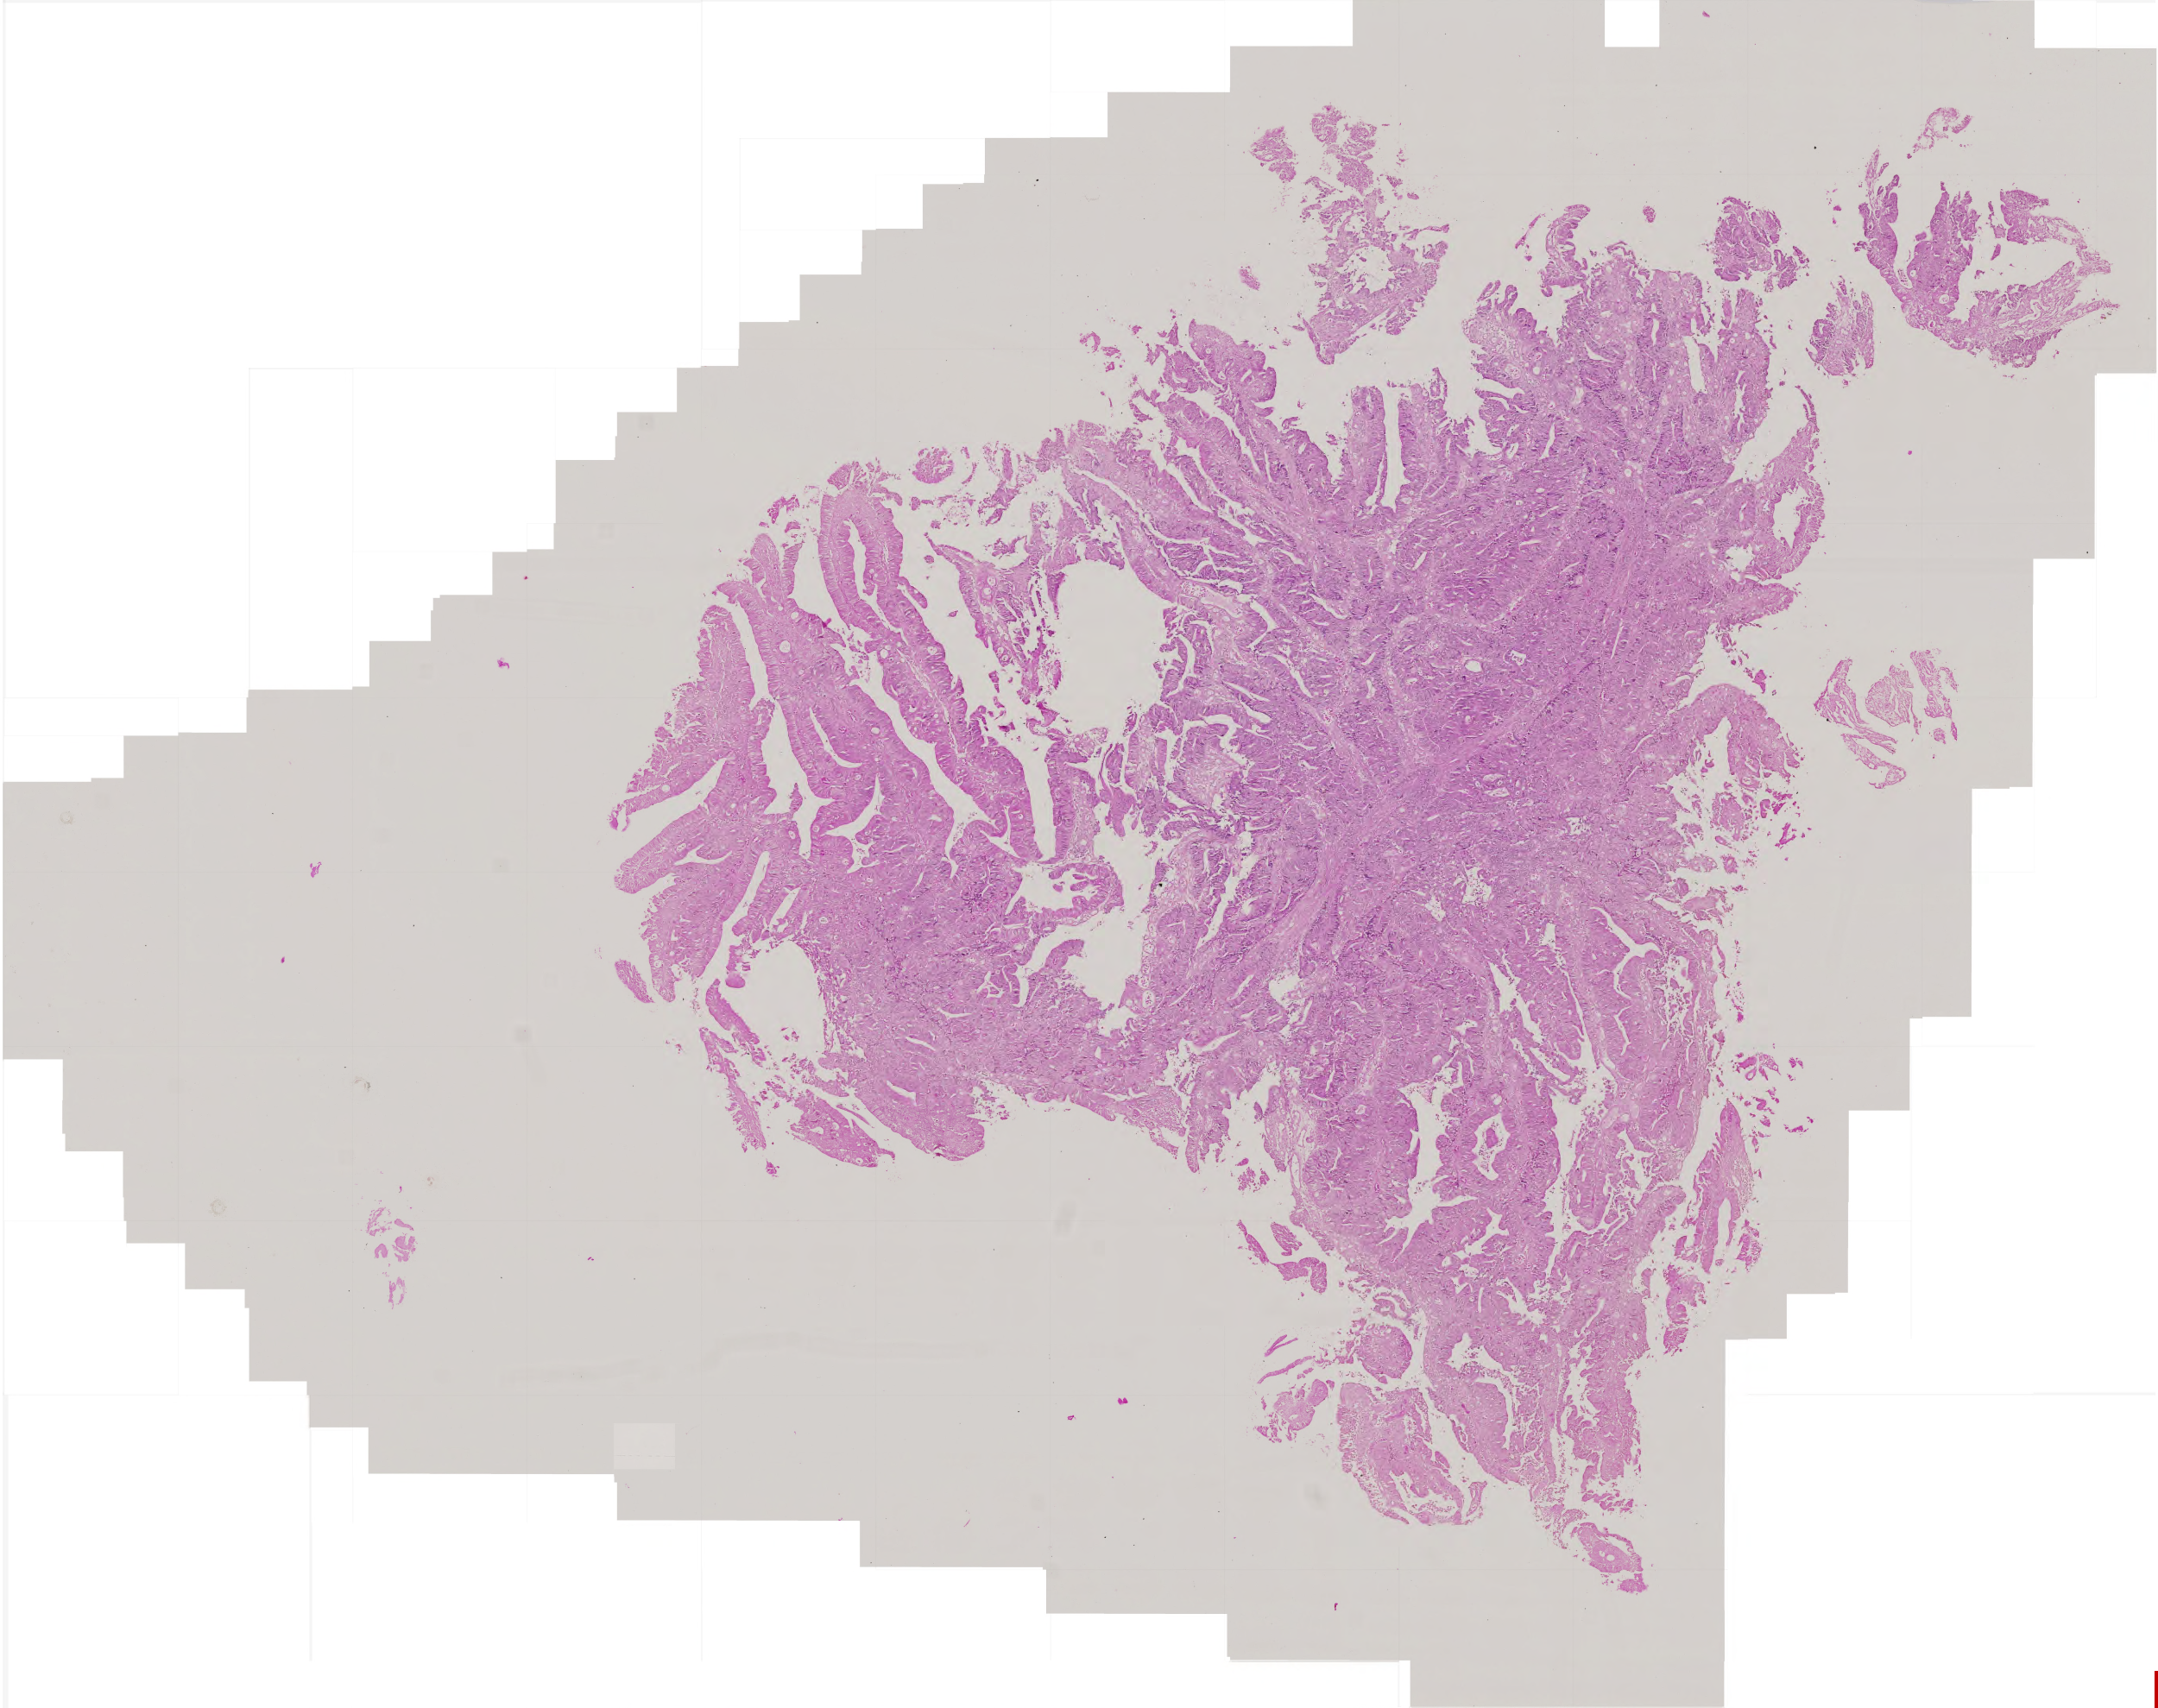
Digitized H&E-stained tissue section (whole slide), a low-resolution overview of the entire scanned area, about 5.0 x 4.0 mm; FFPE section; sample: primary tumour, colon. Male, age 58 years at initial diagnosis.
Lymph nodes positive (case pathology): 15 of 26 examined. Histologic diagnosis: Adenocarcinoma, NOS (rectosigmoid junction). AJCC pathologic stage: IV (5th edition).